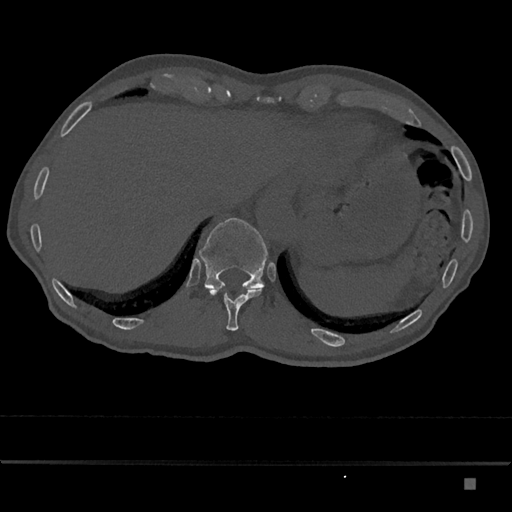
CT including the spine, one axial slice. Position 645 of 797 along the scan axis. Reconstruction kernel Br40s/3. 120 kVp. Bone window (W 1800 / L 400 HU). 512 × 512 image matrix, field of view 390 × 390 mm. Male patient, age 72 years. From the clinical record (not read from this slice): primary cancer: prostate.
Outlined on this slice (semi-automatically segmented with operator editing):
- T11 vertebra: bounding box [x1, y1, x2, y2] px = [209, 287, 263, 331]
- T12 vertebra: [199, 218, 268, 289]